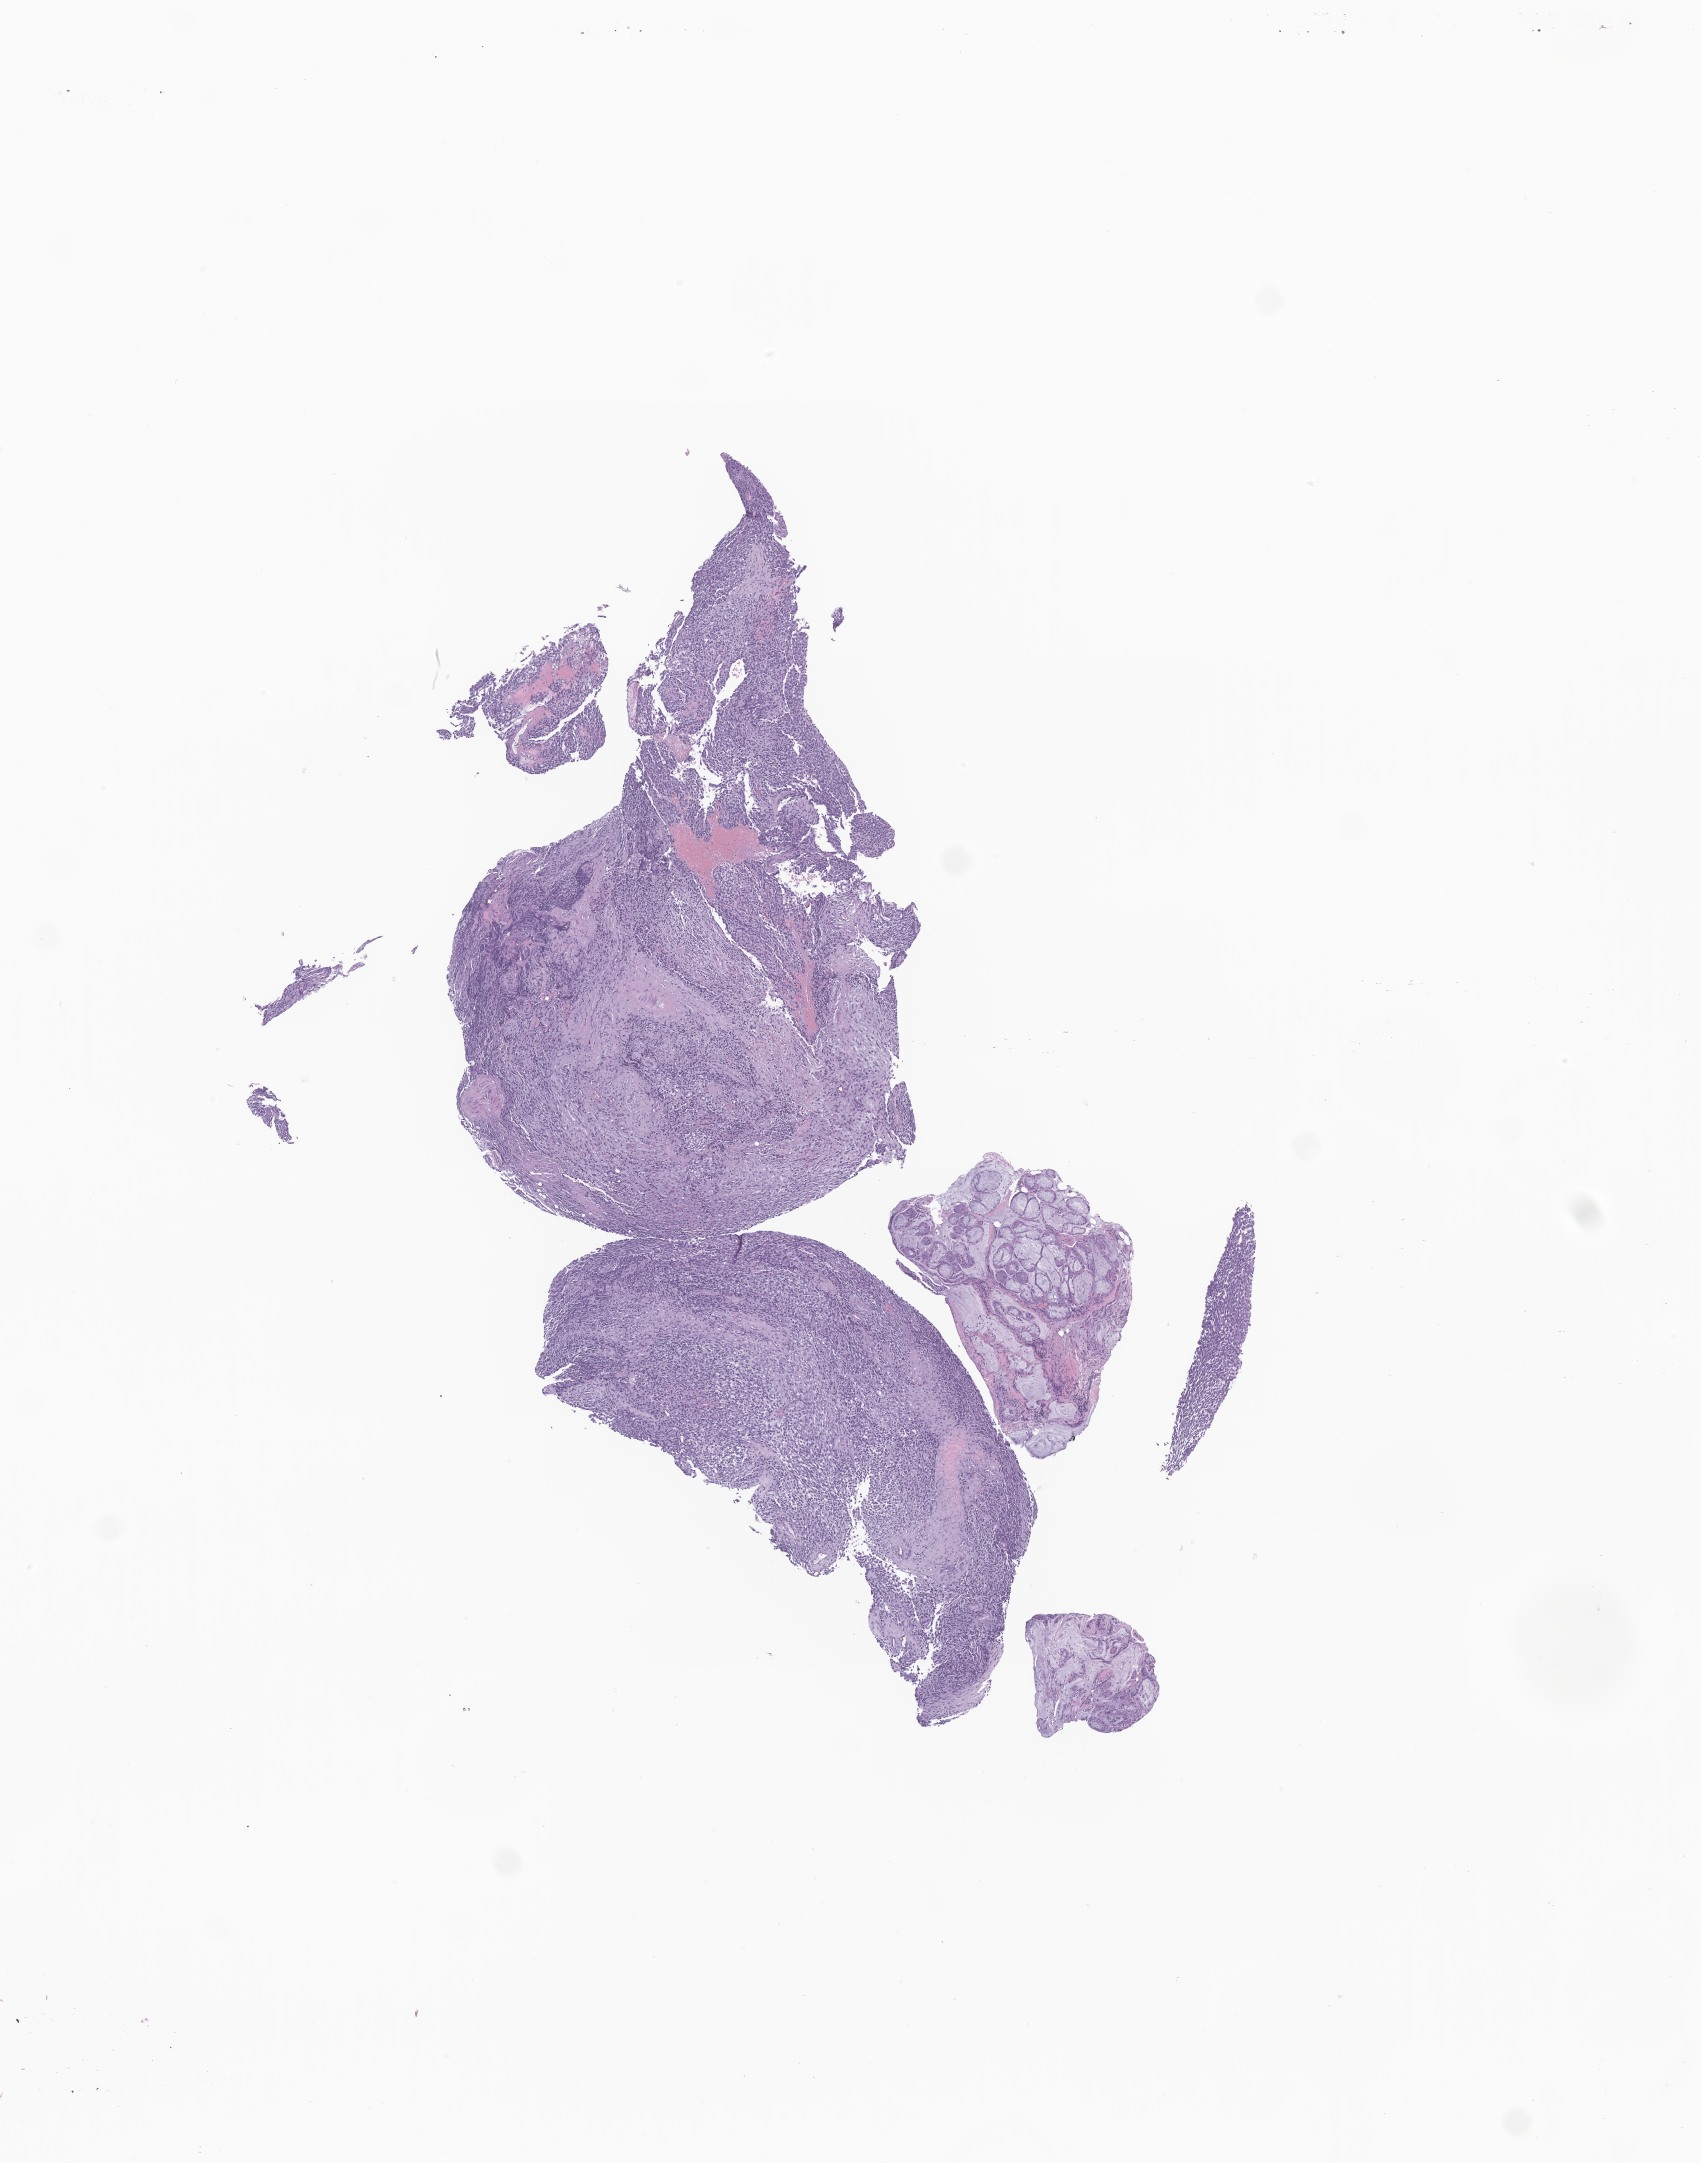
Digitized hematoxylin and eosin (H&E)-stained section of tumor tissue from the cranial and/or facial bone — a low-resolution overview of the entire scanned area, about 7.2 x 9.1 mm; FFPE section. Patient: female, age 86 months.
Tissue or organ of origin (case record): bones of skull and face and associated joints. Diagnosis (ICD-O-3 morphology term): Chordoma, NOS.